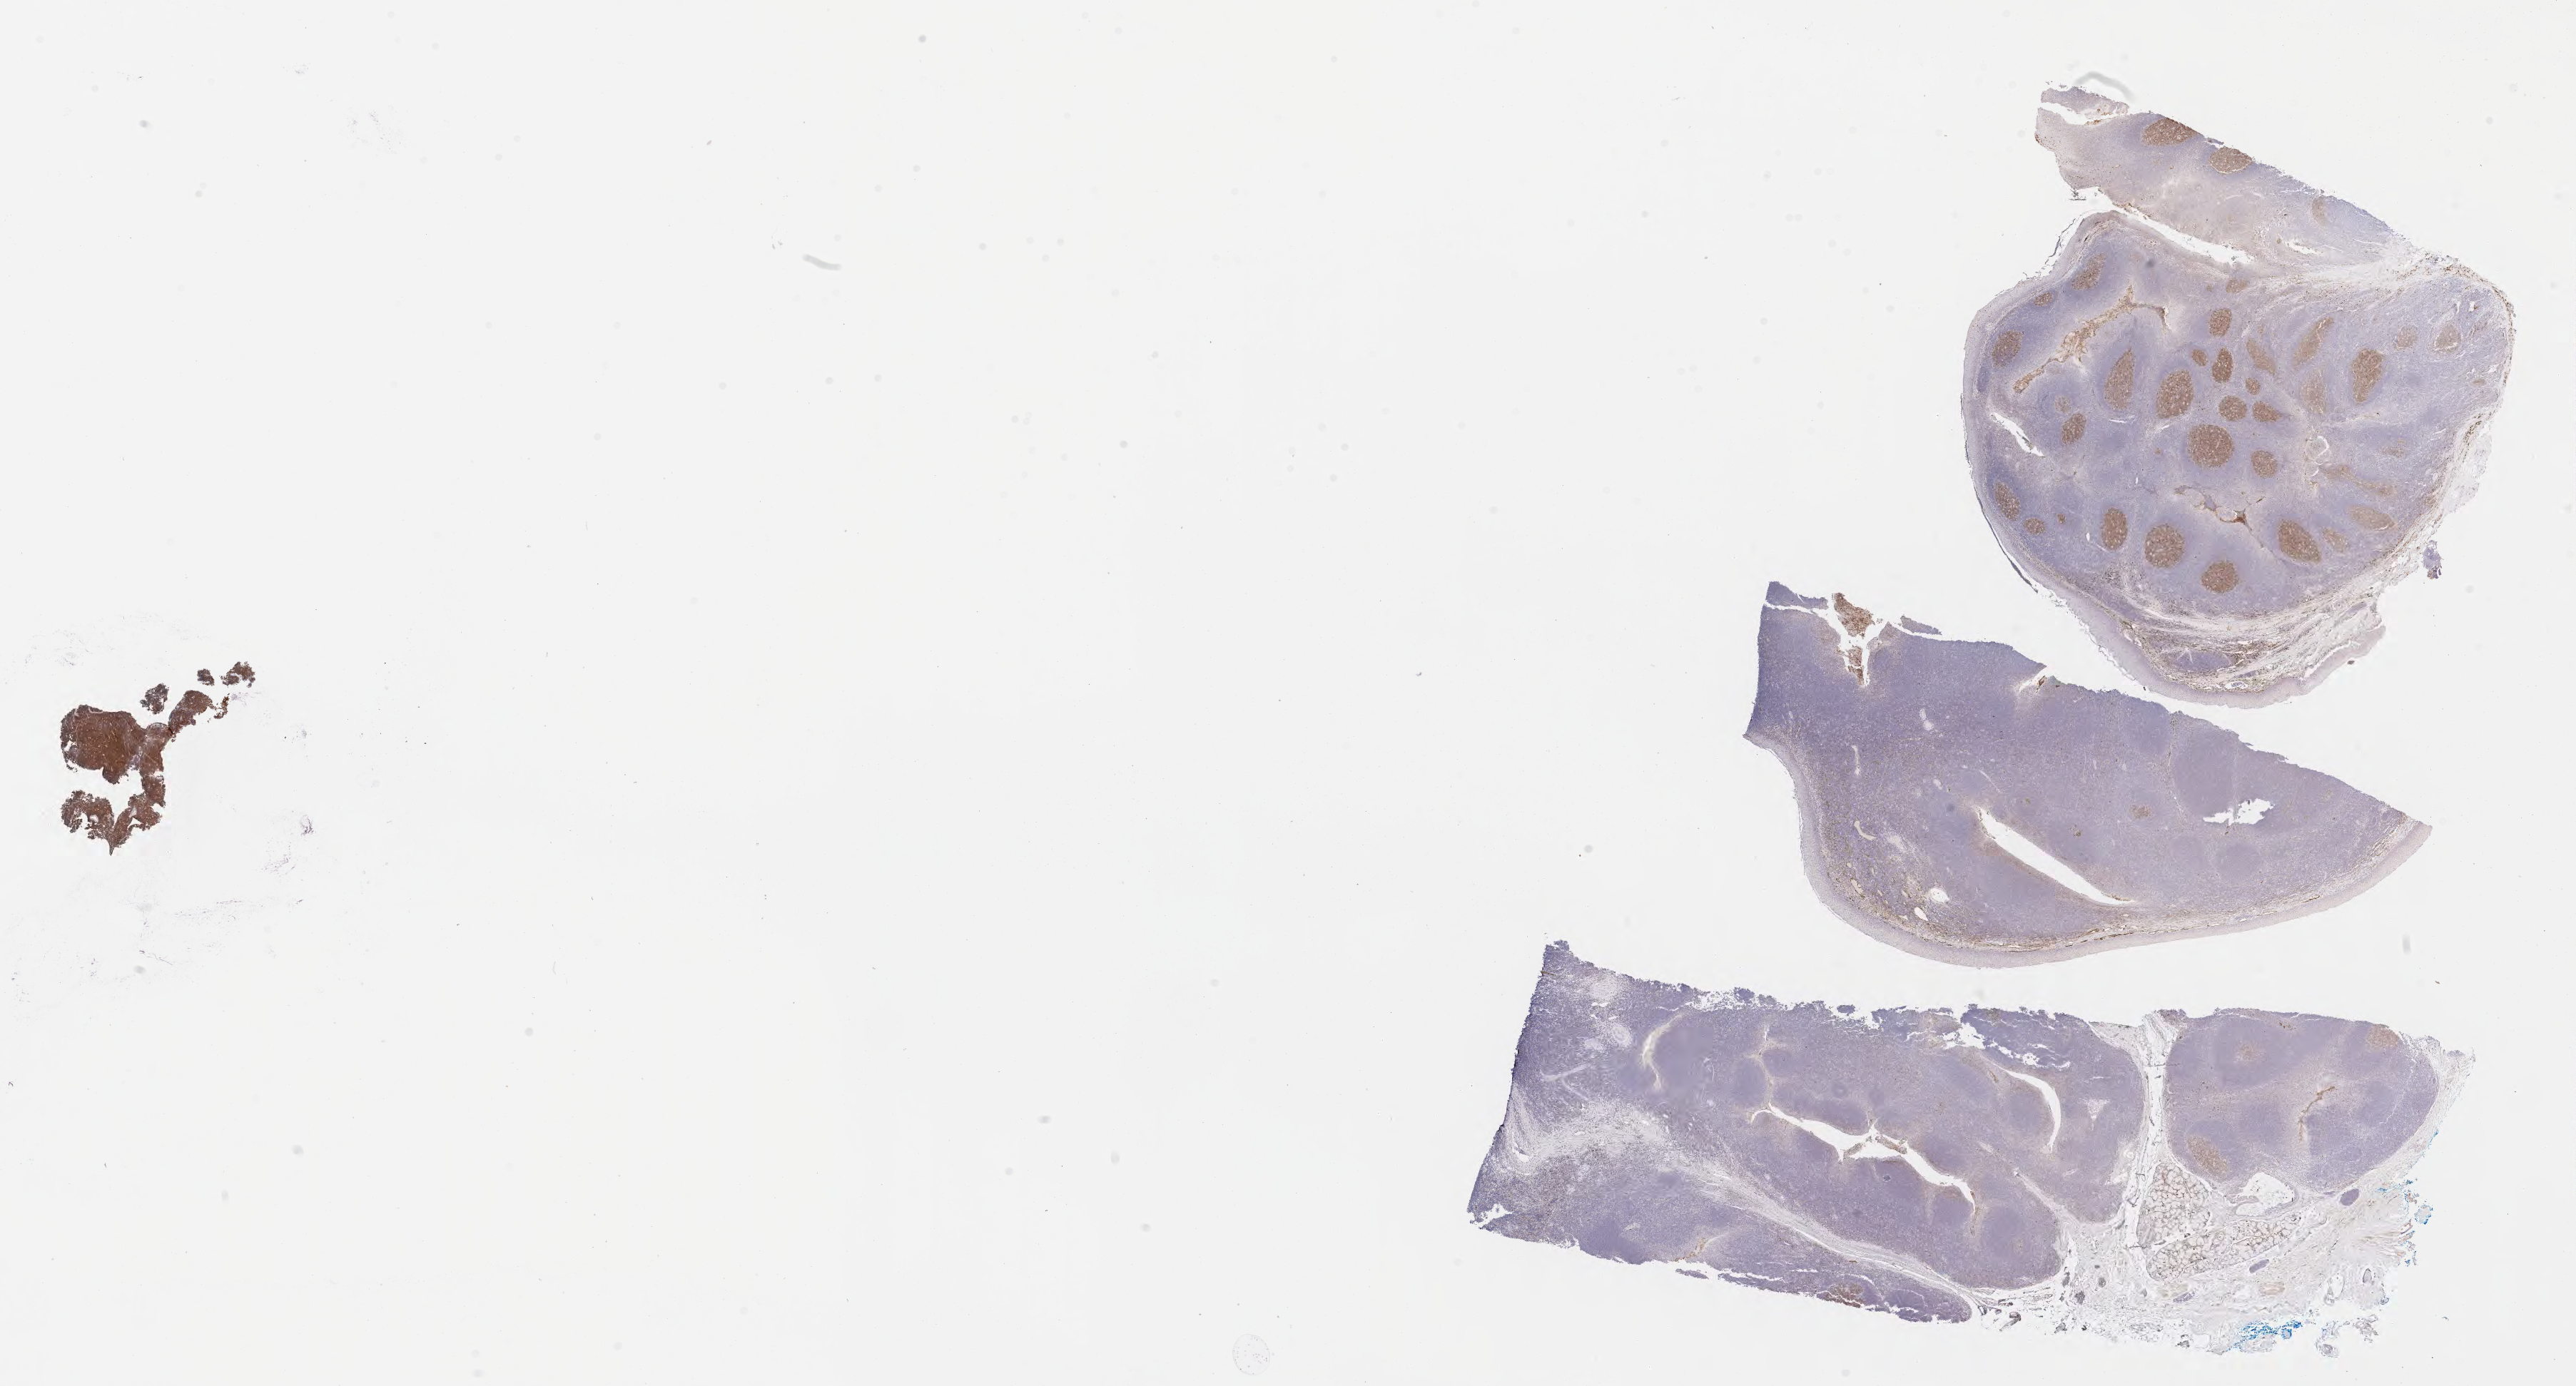
Immunohistochemistry (IHC) whole-slide image stained for CD10 — a low-resolution overview of the entire scanned area, about 29.2 x 15.7 mm; tumor tissue. Male patient; age at initial diagnosis 8 years.
- diagnosis: Burkitt lymphoma, NOS